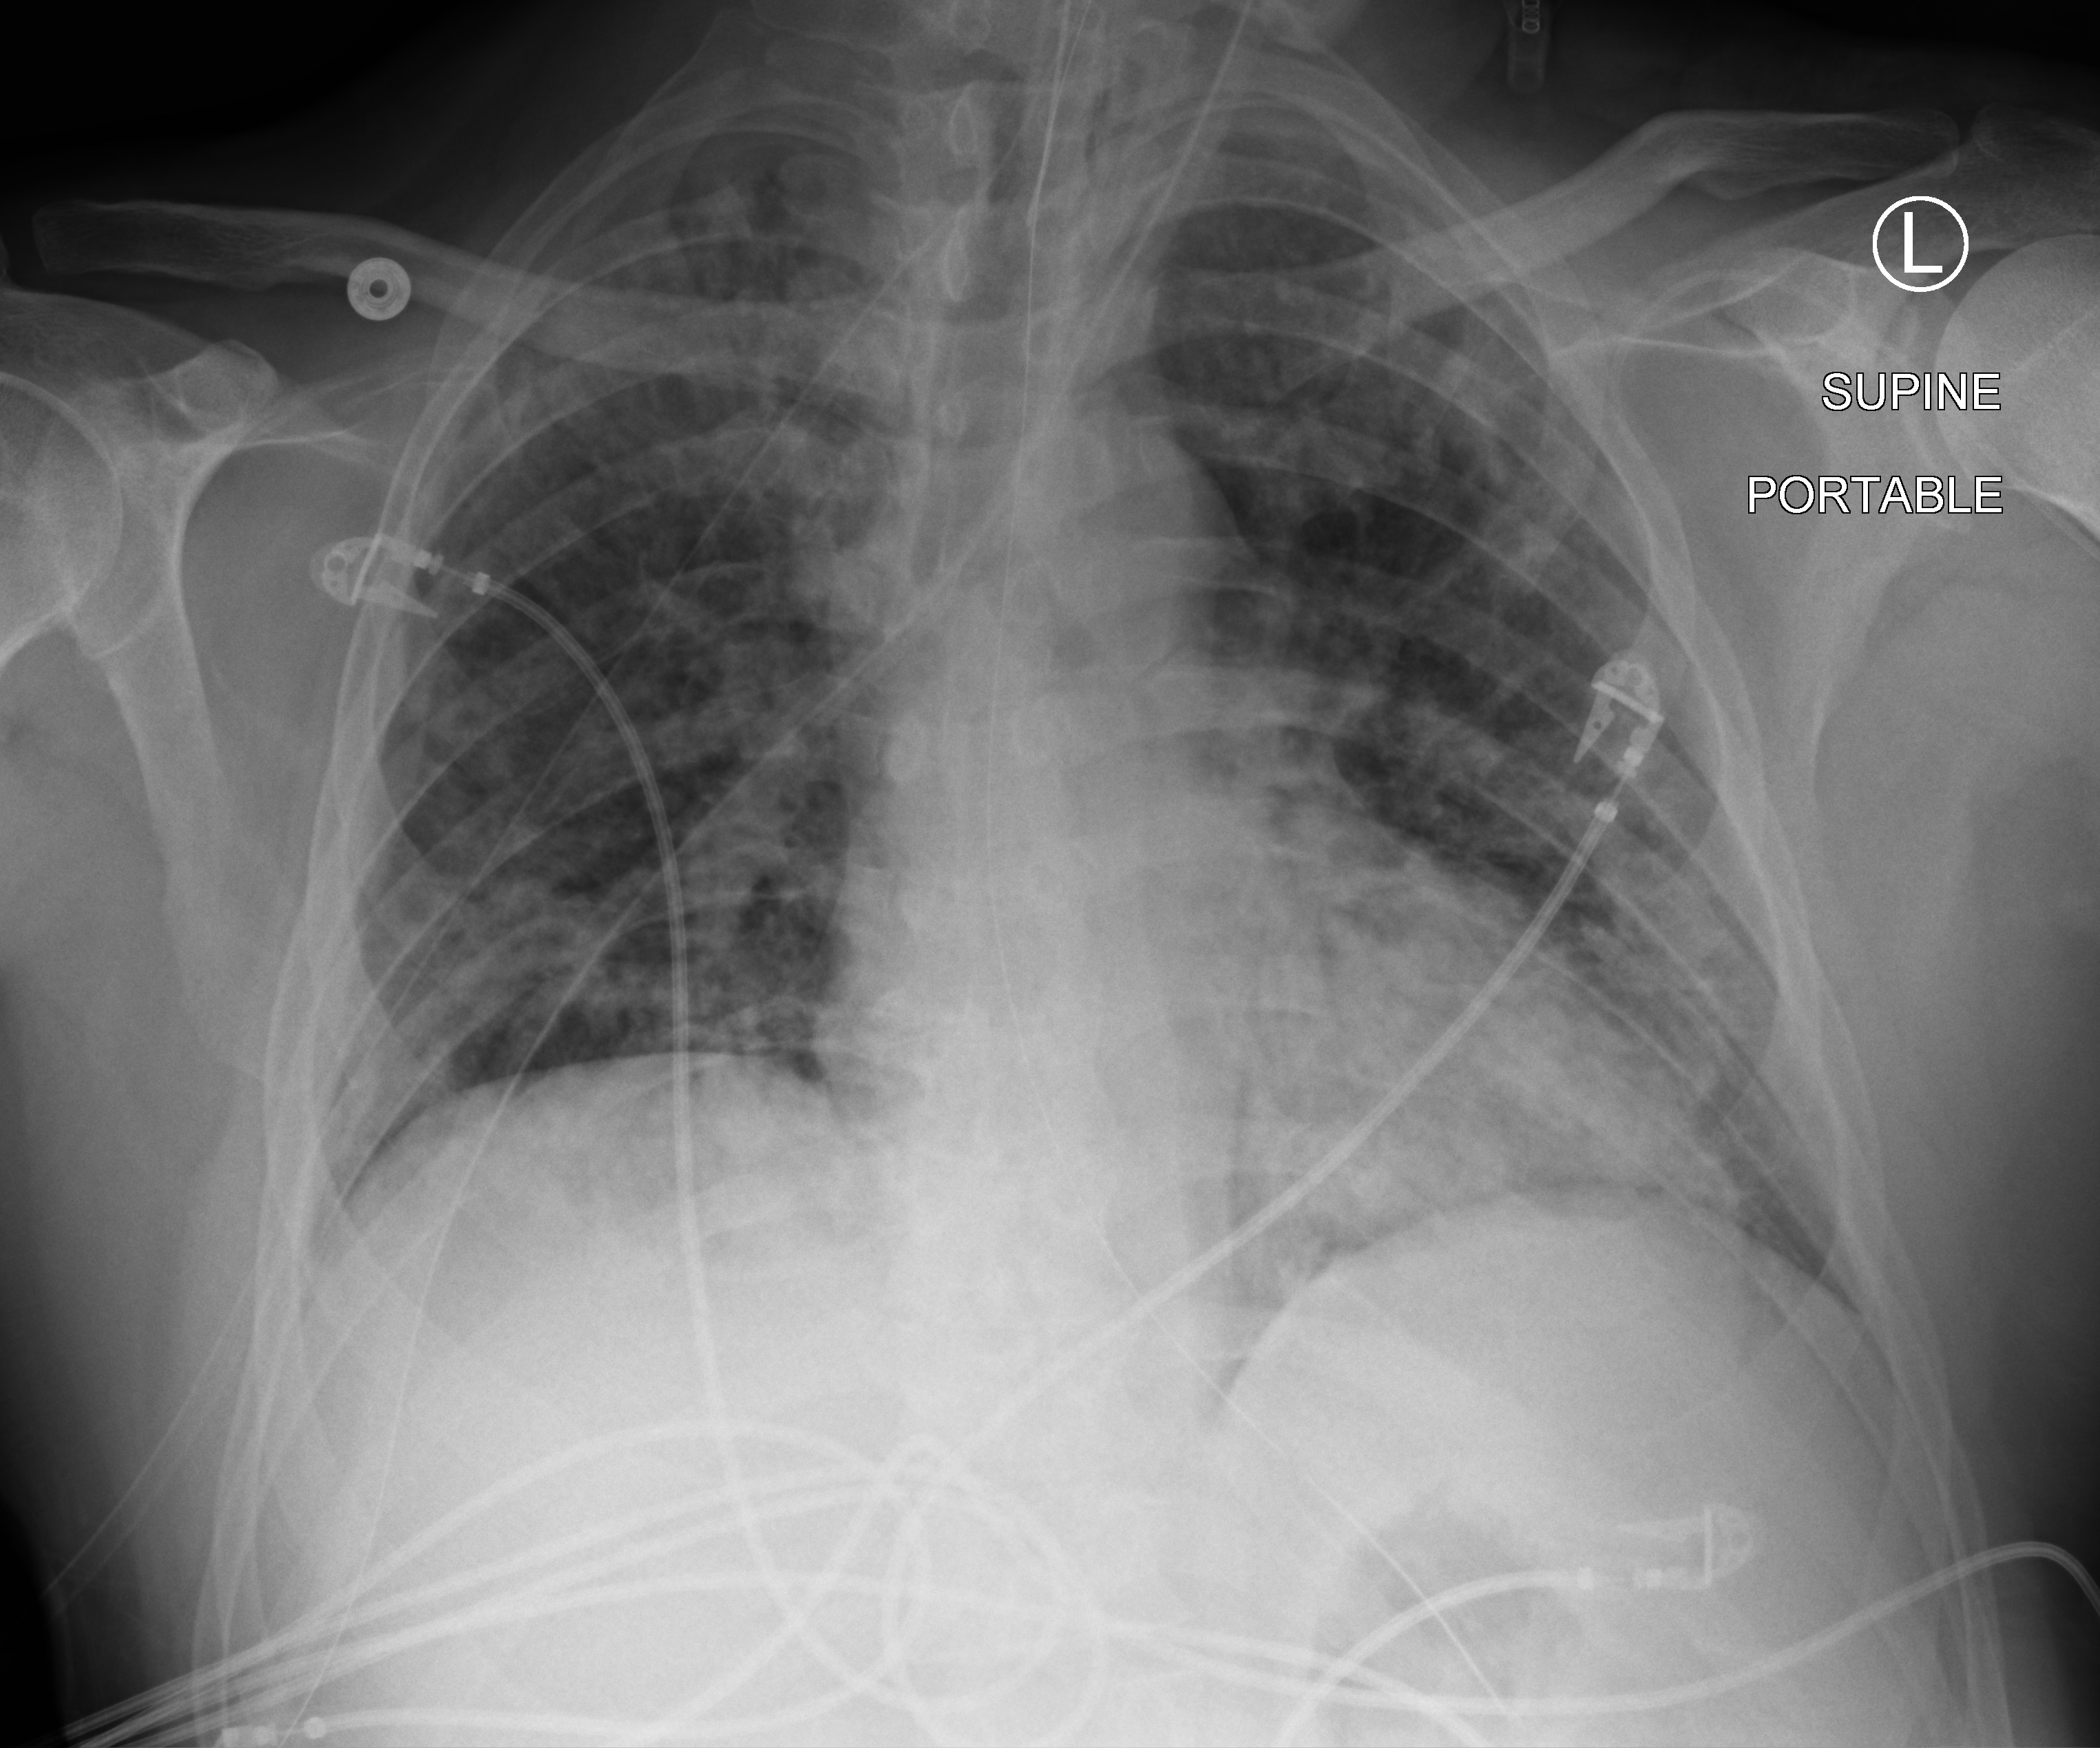
Portable chest radiograph, anteroposterior (AP) projection. Patient hospitalised with COVID-19; male, aged 18–59 years.
Admission-level facts for this patient (not findings on this image; timing relative to this image not recorded):
- mechanically ventilated during this hospital stay: yes